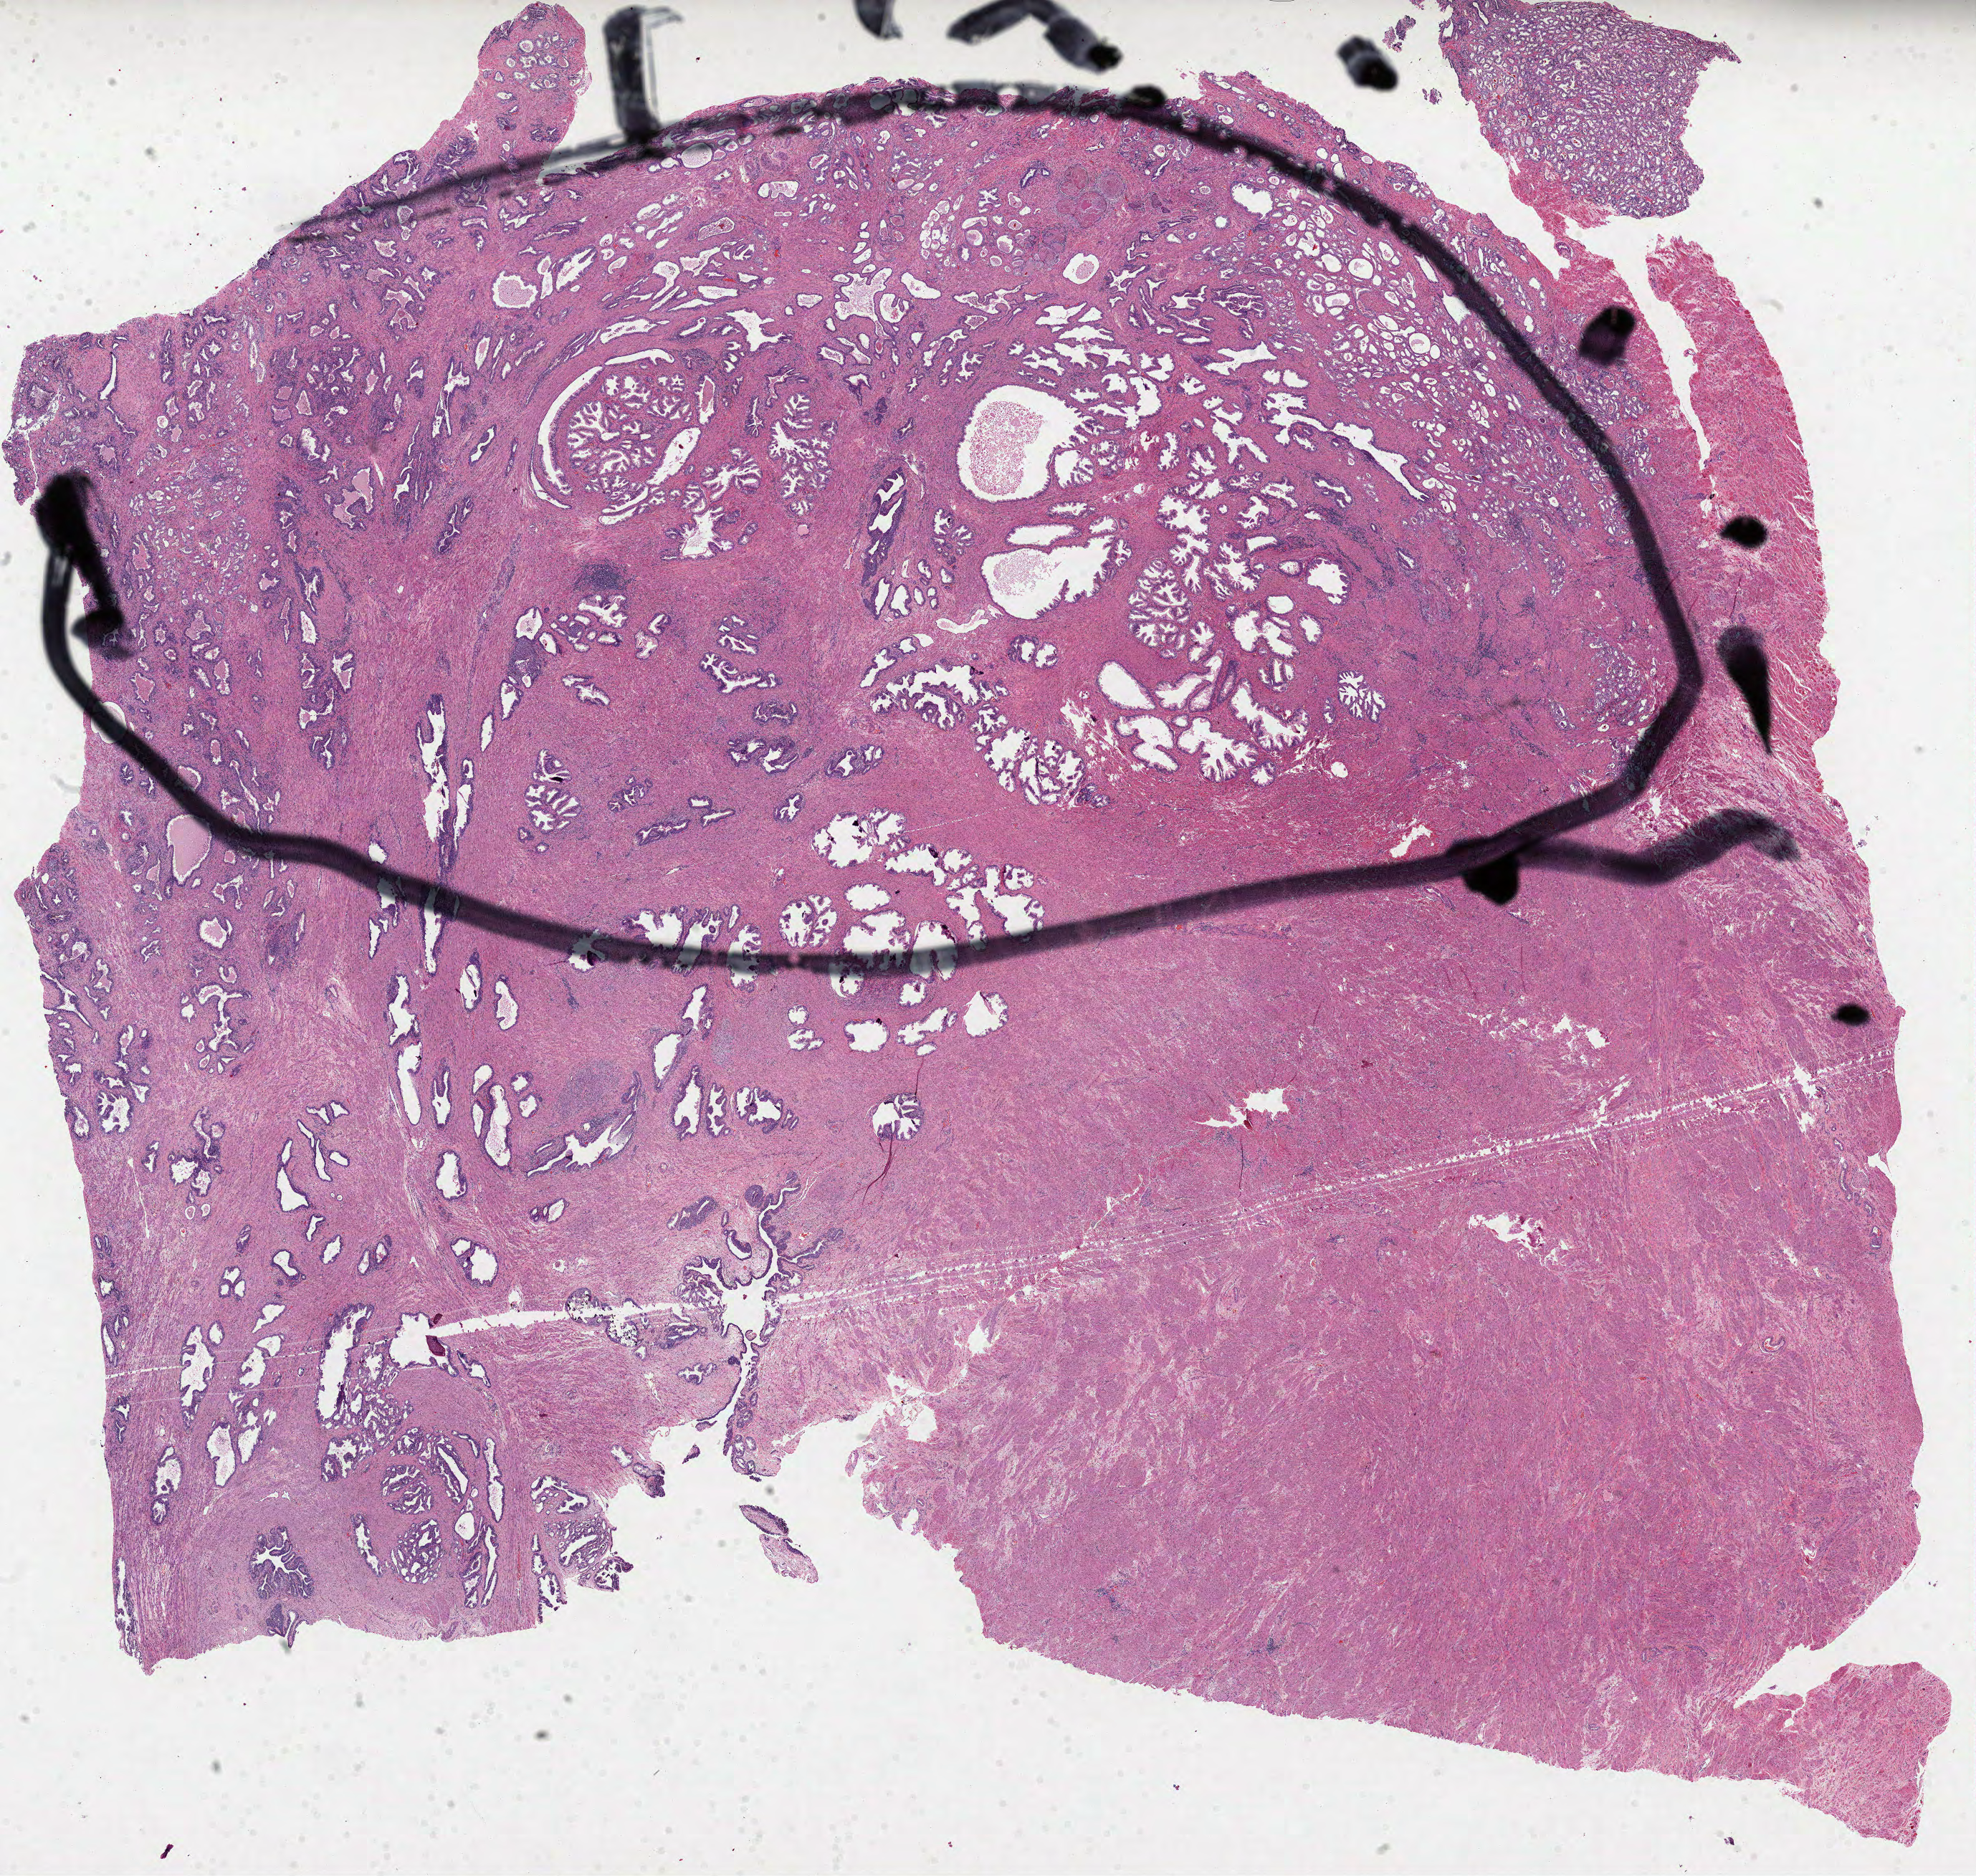
H&E whole-slide image, whole scanned area (about 22.2 x 21.1 mm, from a 40x scan) shown as a low-resolution overview. Formalin-fixed paraffin-embedded (FFPE) diagnostic section. Sample: primary tumour, prostate. Male, age 50 years at initial diagnosis. Gleason score: 7 (4+3).
Pathologic diagnosis: Acinar cell carcinoma (prostate gland). Laterality: bilateral.